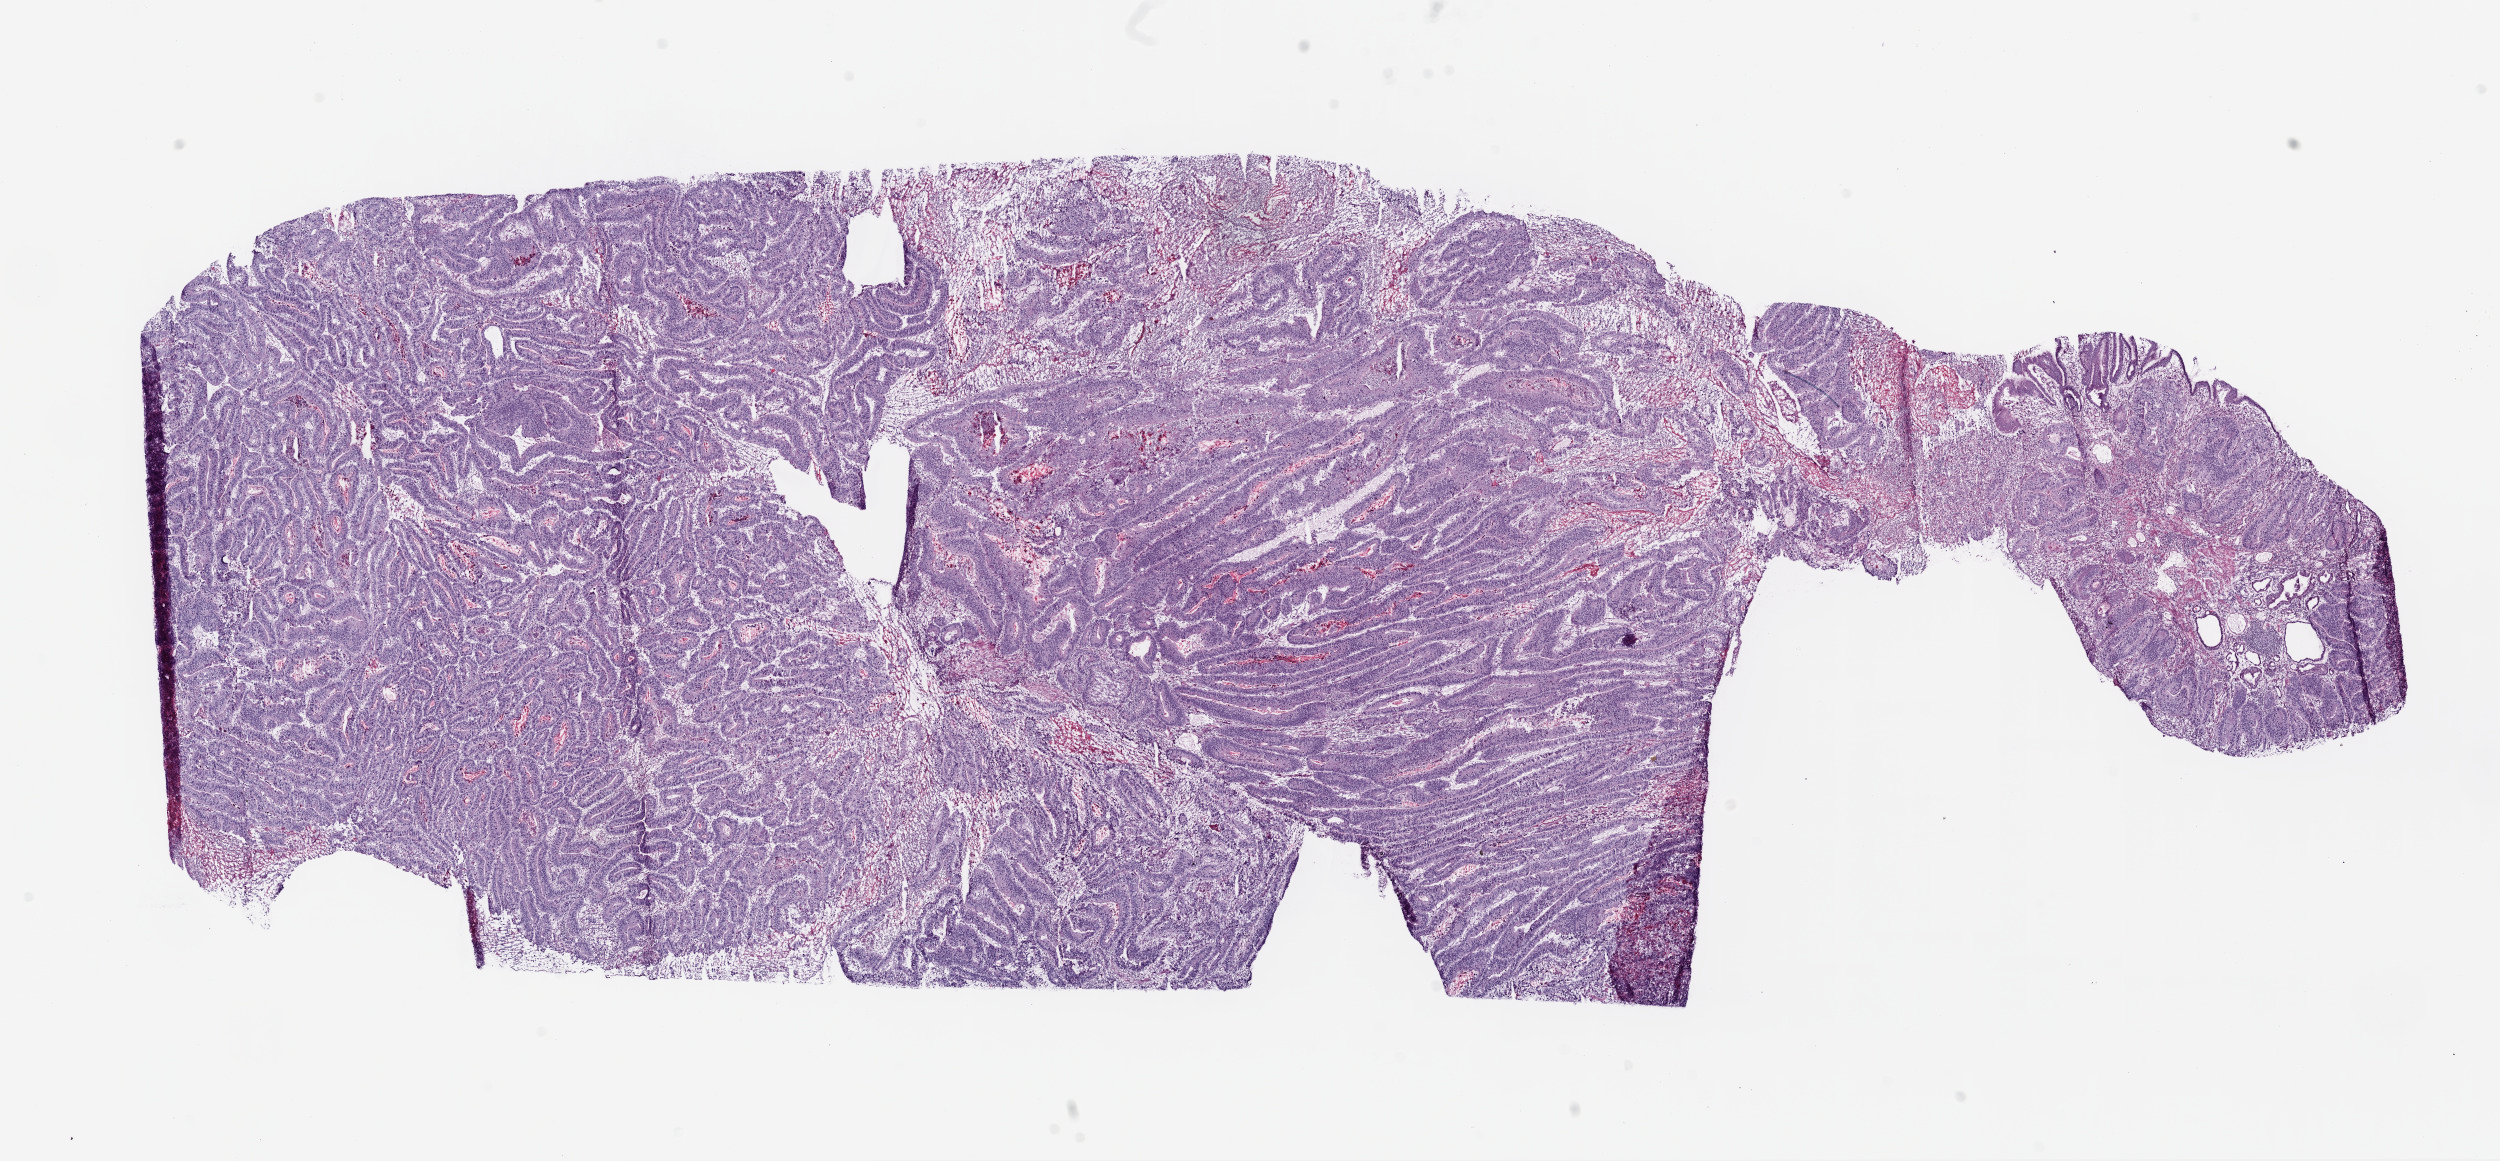
Whole-slide histology image, H&E-stained — a low-resolution overview of the entire scanned area, about 20.1 x 9.3 mm (slide scanned at 20x); frozen section from the bottom of the tissue portion; sample: primary tumour, stomach. Patient: male, age at initial diagnosis 57 years. Histologic grade: G2 (moderately differentiated). Slide review estimates, as recorded: tumour cells 75%, tumour nuclei 80%, normal cells 10%, stromal cells 10%, necrosis 5%.
* AJCC pathologic stage: IB
* histologic diagnosis: Adenocarcinoma, intestinal type